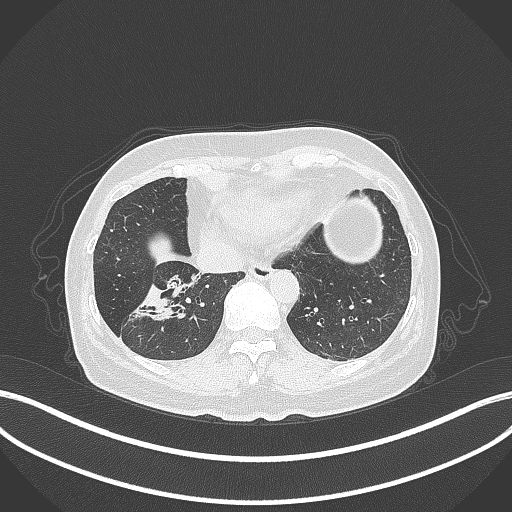
Chest CT, one axial slice. Slice 110 of 429 in the series (ordered by position). Reconstruction kernel B70f. Lung window (W 1500 / L -600 HU). 512 × 512 image matrix, field of view 400 × 400 mm. Patient: female, 67 years. Case-level facts recorded for this patient, not image findings: clinical TNM (as recorded): T1c N1 M0; histopathological grade: G2-3.
Outlined on this slice (bounding box drawn by a radiologist):
- lung tumour (recorded histology: adenocarcinoma): bounding box (x1, y1, x2, y2) in pixels: (137, 280, 196, 322)